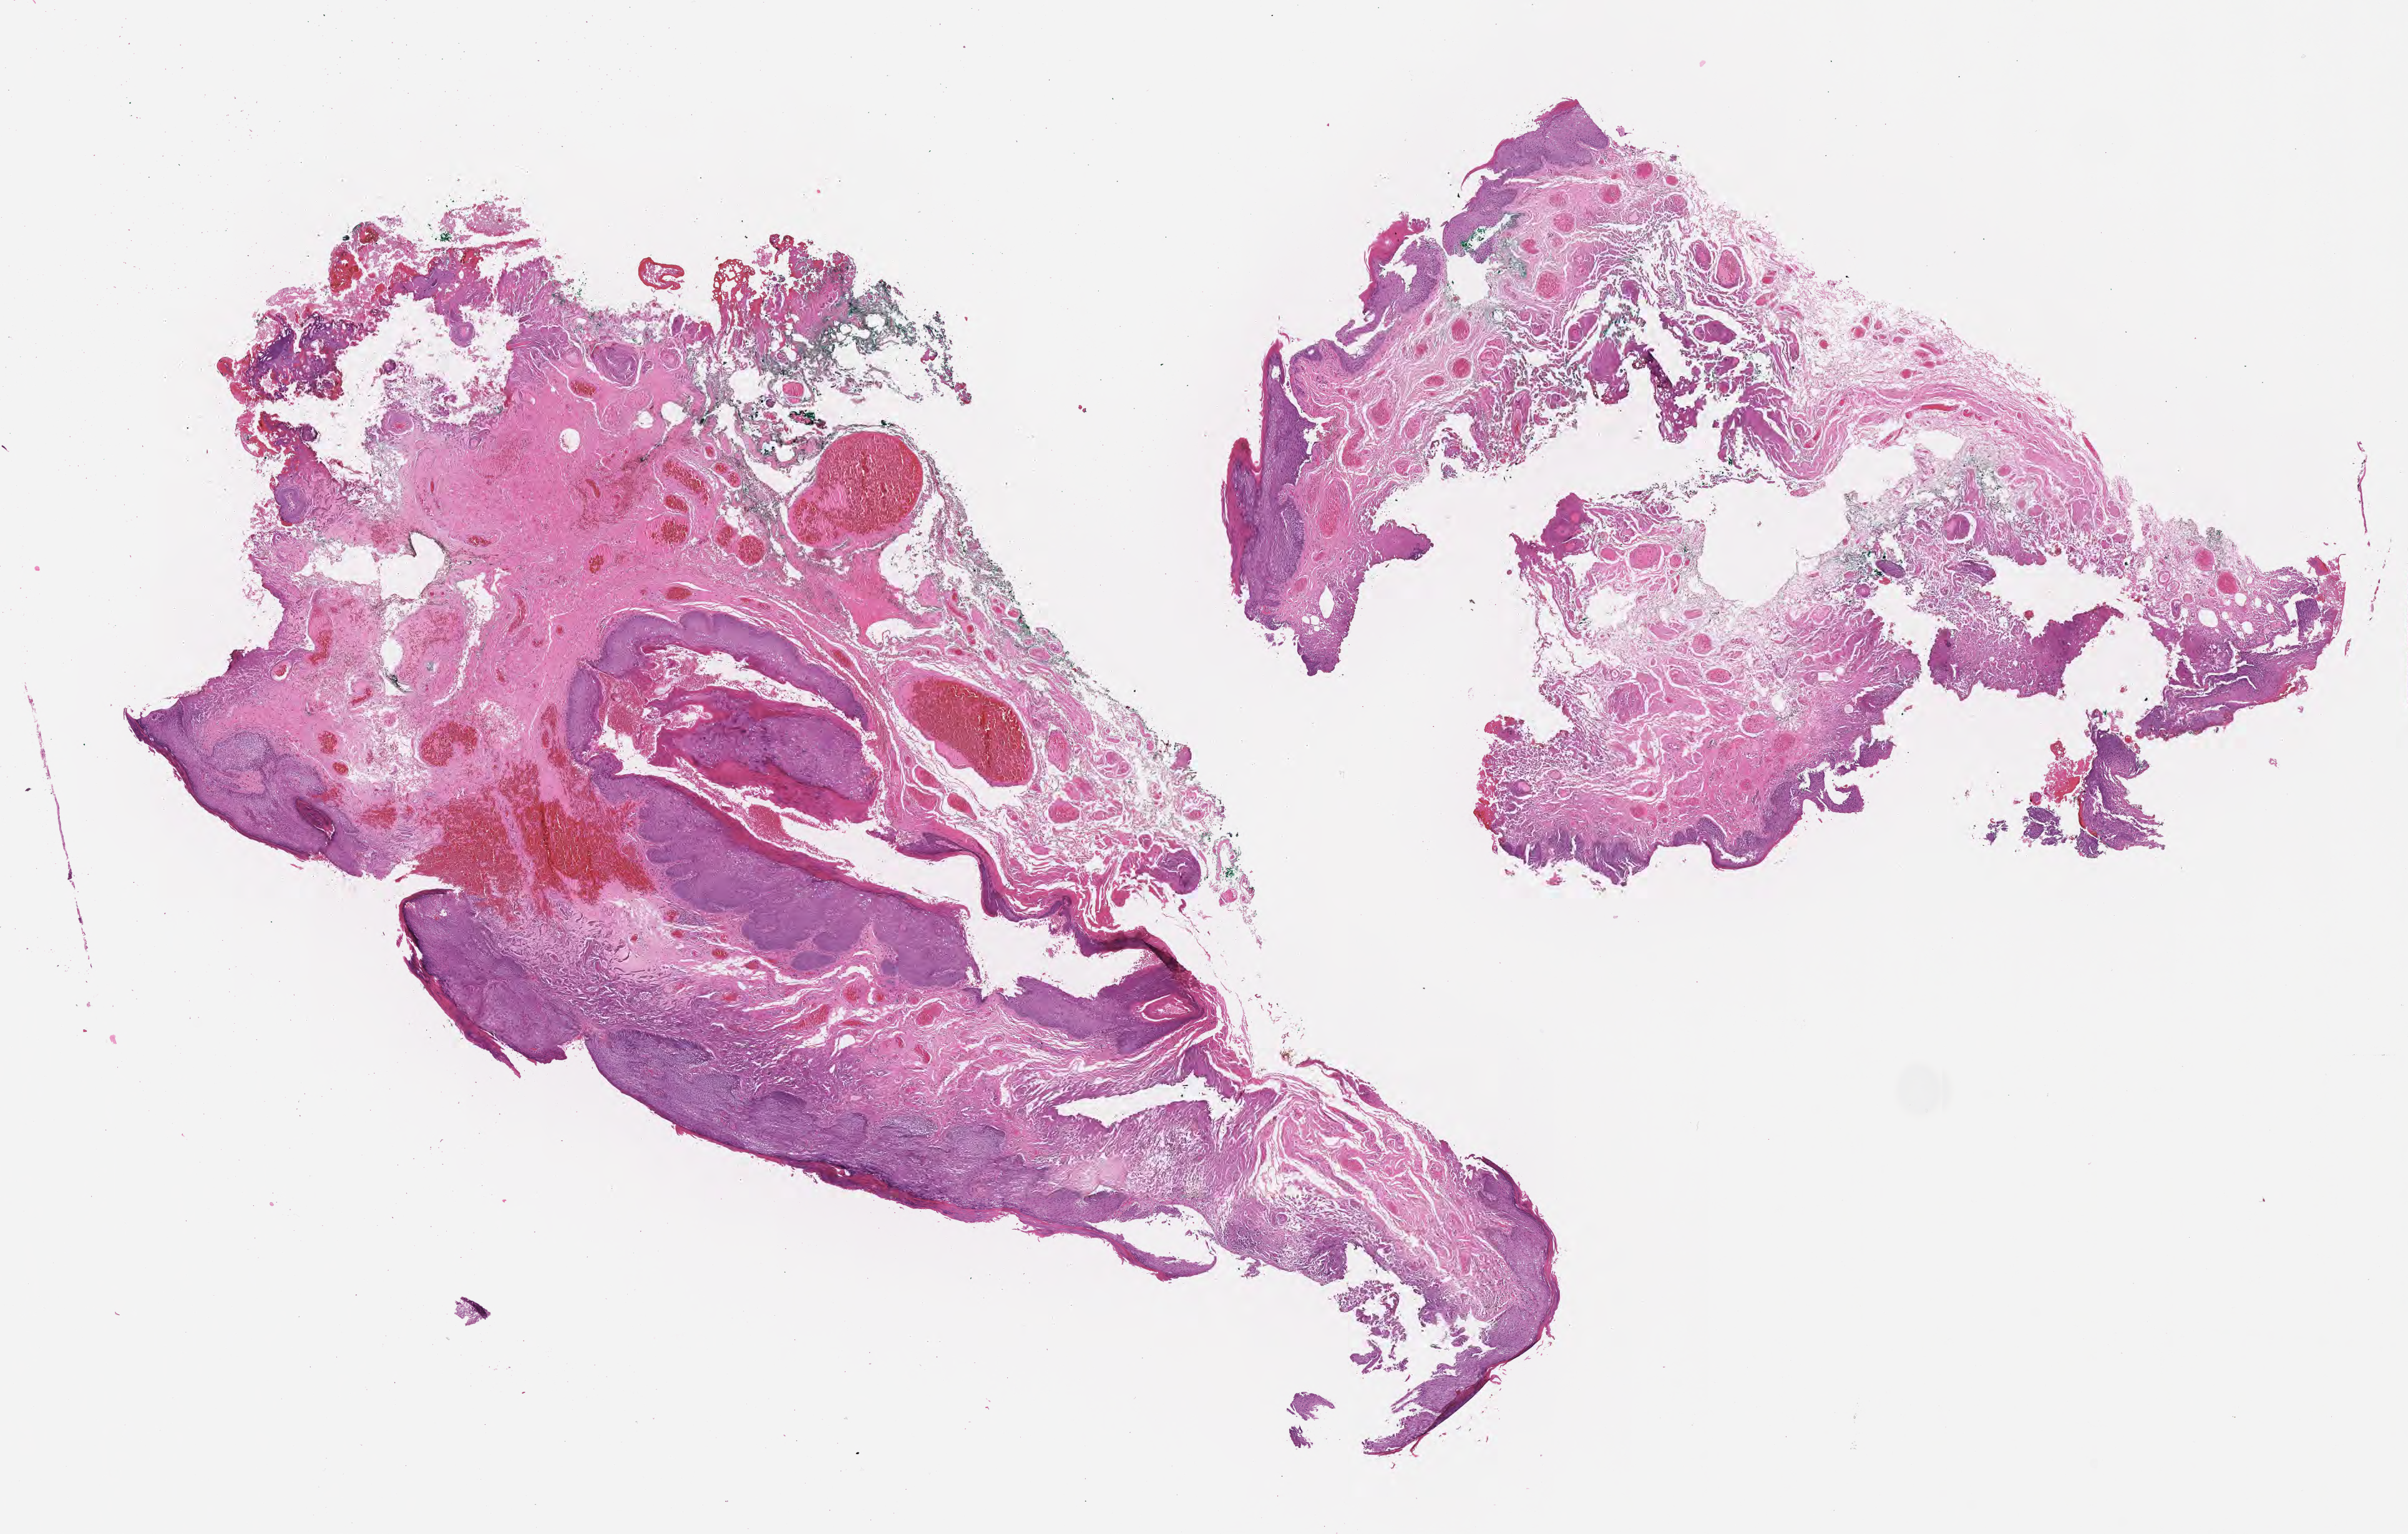
Whole-slide image, haematoxylin and eosin stain, a low-resolution overview of the entire scanned area, about 15.6 x 9.9 mm; formalin-fixed paraffin-embedded section; specimen: normal-tissue sample (non-tumor) from a patient with burkitt lymphoma, NOS. Male patient, age 46 years.
This section: non-tumor tissue sample; the patient's diagnosis is given above. Section: bottom of the tissue portion.